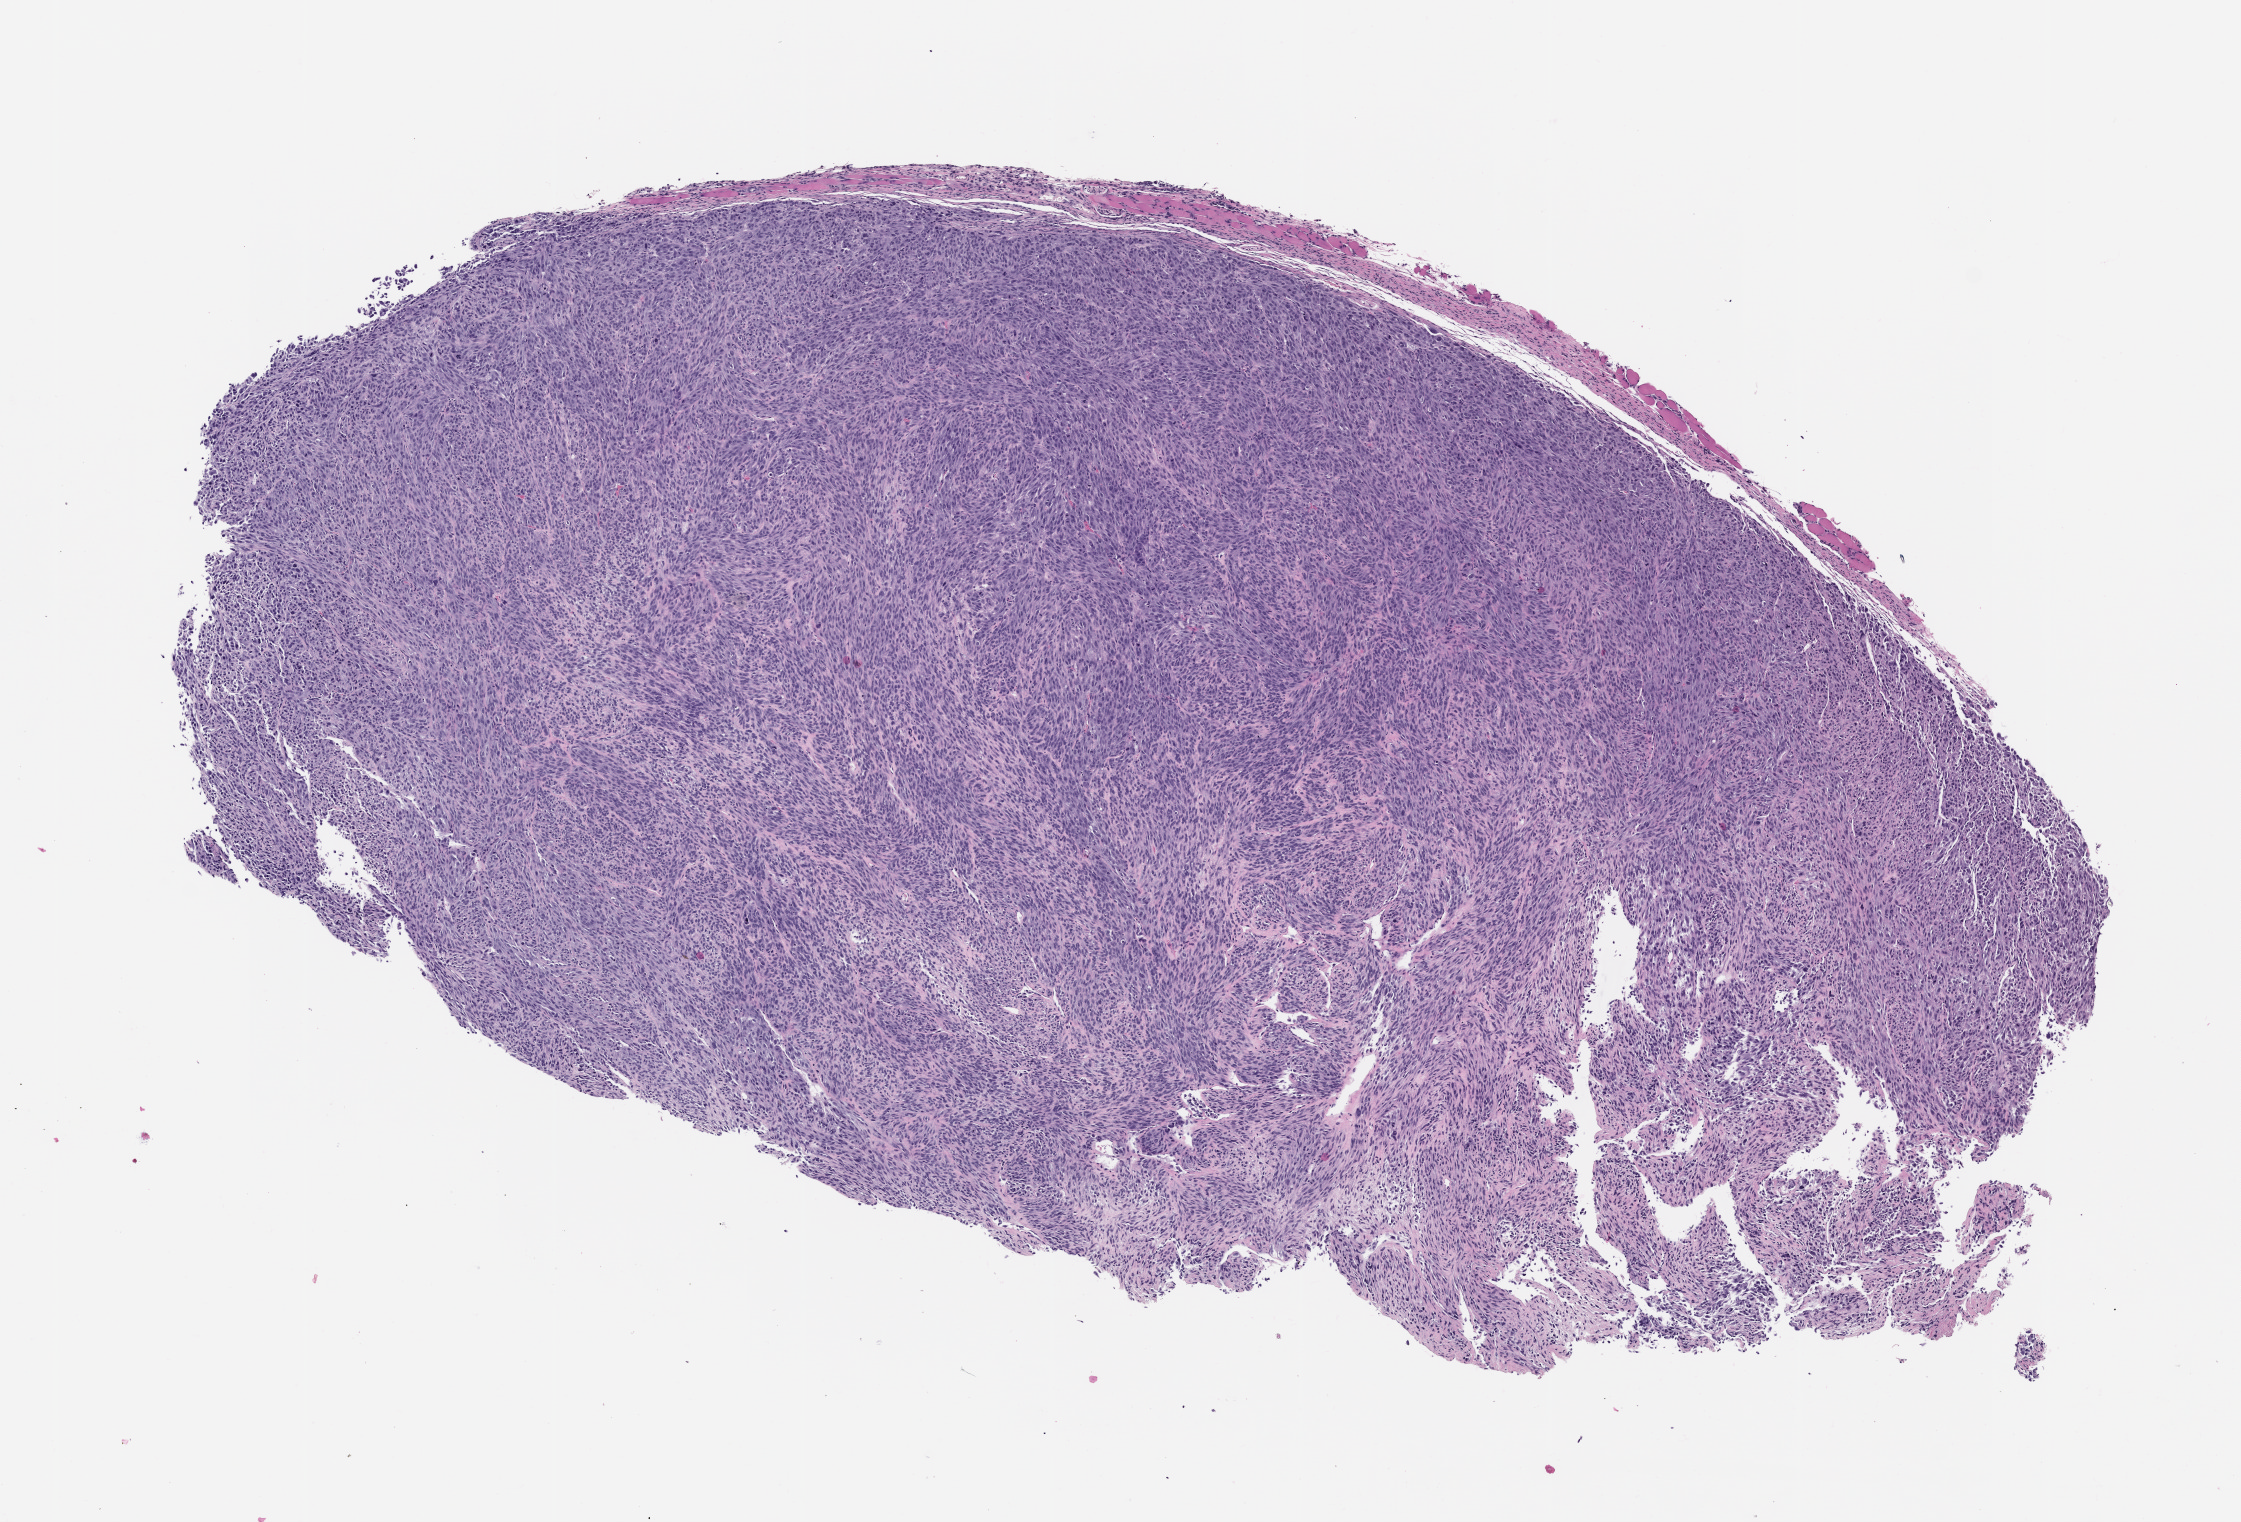
Whole-slide image, haematoxylin and eosin: patient-derived xenograft (human tumor grown in a mouse), passage 2, low-resolution overview of the scanned area, about 9.0 x 6.1 mm, formalin-fixed, paraffin-embedded (FFPE) tissue, tumor site category: bone.
Originating patient diagnosis: Osteosarcoma.